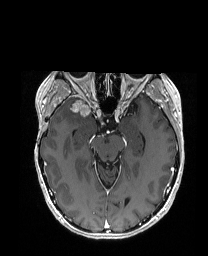
Brain MRI from a brain-tumour surgery series, one axial slice; position 111 of 192 along the scan axis; T1-weighted post-contrast; 1 mm slice thickness; 208 × 256 image matrix, field of view 203 × 250 mm. From the clinical record (not read from this slice): histopathology: Metastatic Carcinoma from Breast primary; tumour location: Right Frontal.
Annotated regions visible in this slice (expert manual segmentation):
- tumour: box from (x=67, y=98) to (x=88, y=114) px